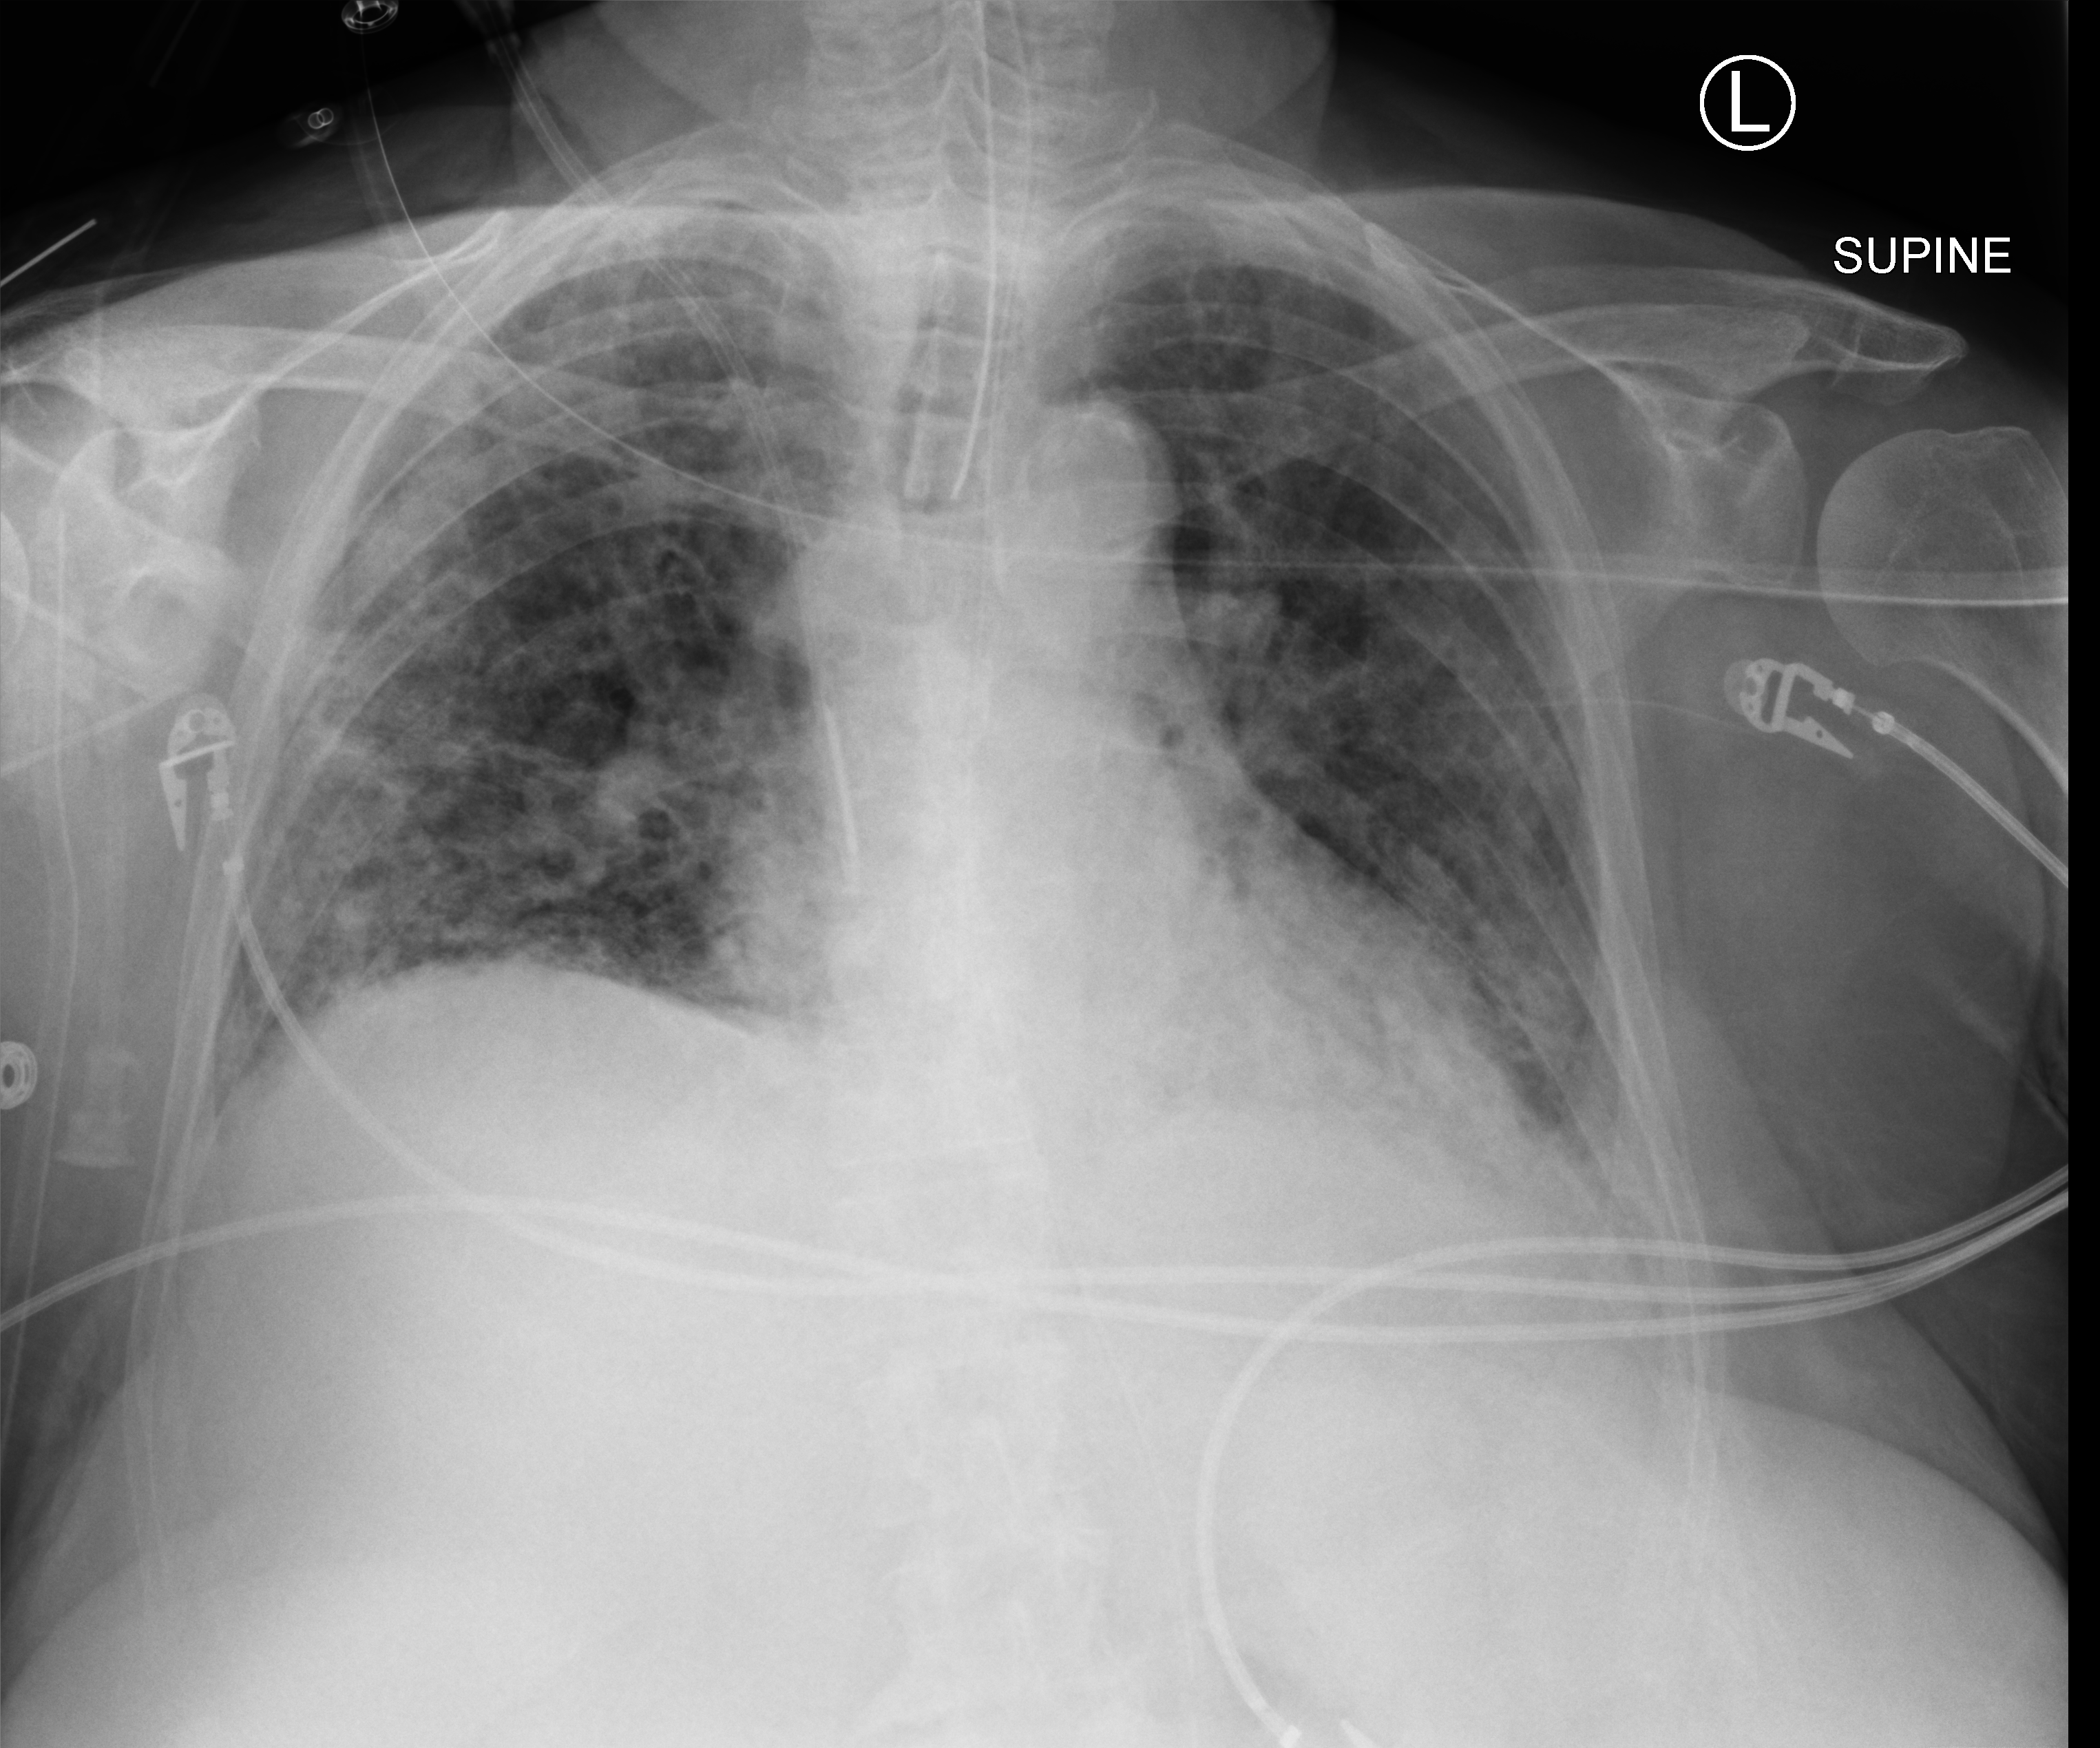
Chest X-ray (portable). Female patient hospitalised with COVID-19, age 75–90 years.
From the hospital-stay record, not from the radiograph (when in the stay this image was taken is not recorded): admitted to intensive care during this hospital stay: yes.